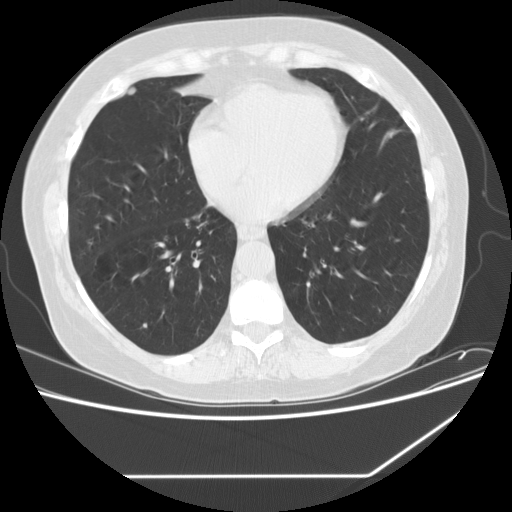
Low-dose screening chest CT, axial slice; second annual screen; lung window (W 1500 / L -600 HU); standard (soft-tissue) reconstruction kernel (STANDARD). Female participant, aged 59 years at enrolment. Current smoker at enrolment.
Expert-annotated lung lesion, bounding box [x1, y1, x2, y2] px = [125, 308, 164, 344]. No non-calcified nodule or mass ≥4 mm was recorded by the screening reader at this exam. Participant outcome: lung cancer diagnosed 380 days after this screen (after the third annual screen) — non-small cell carcinoma, right lower lobe, poorly differentiated (G3), stage IA (AJCC 6th edition), 15 mm at pathology.